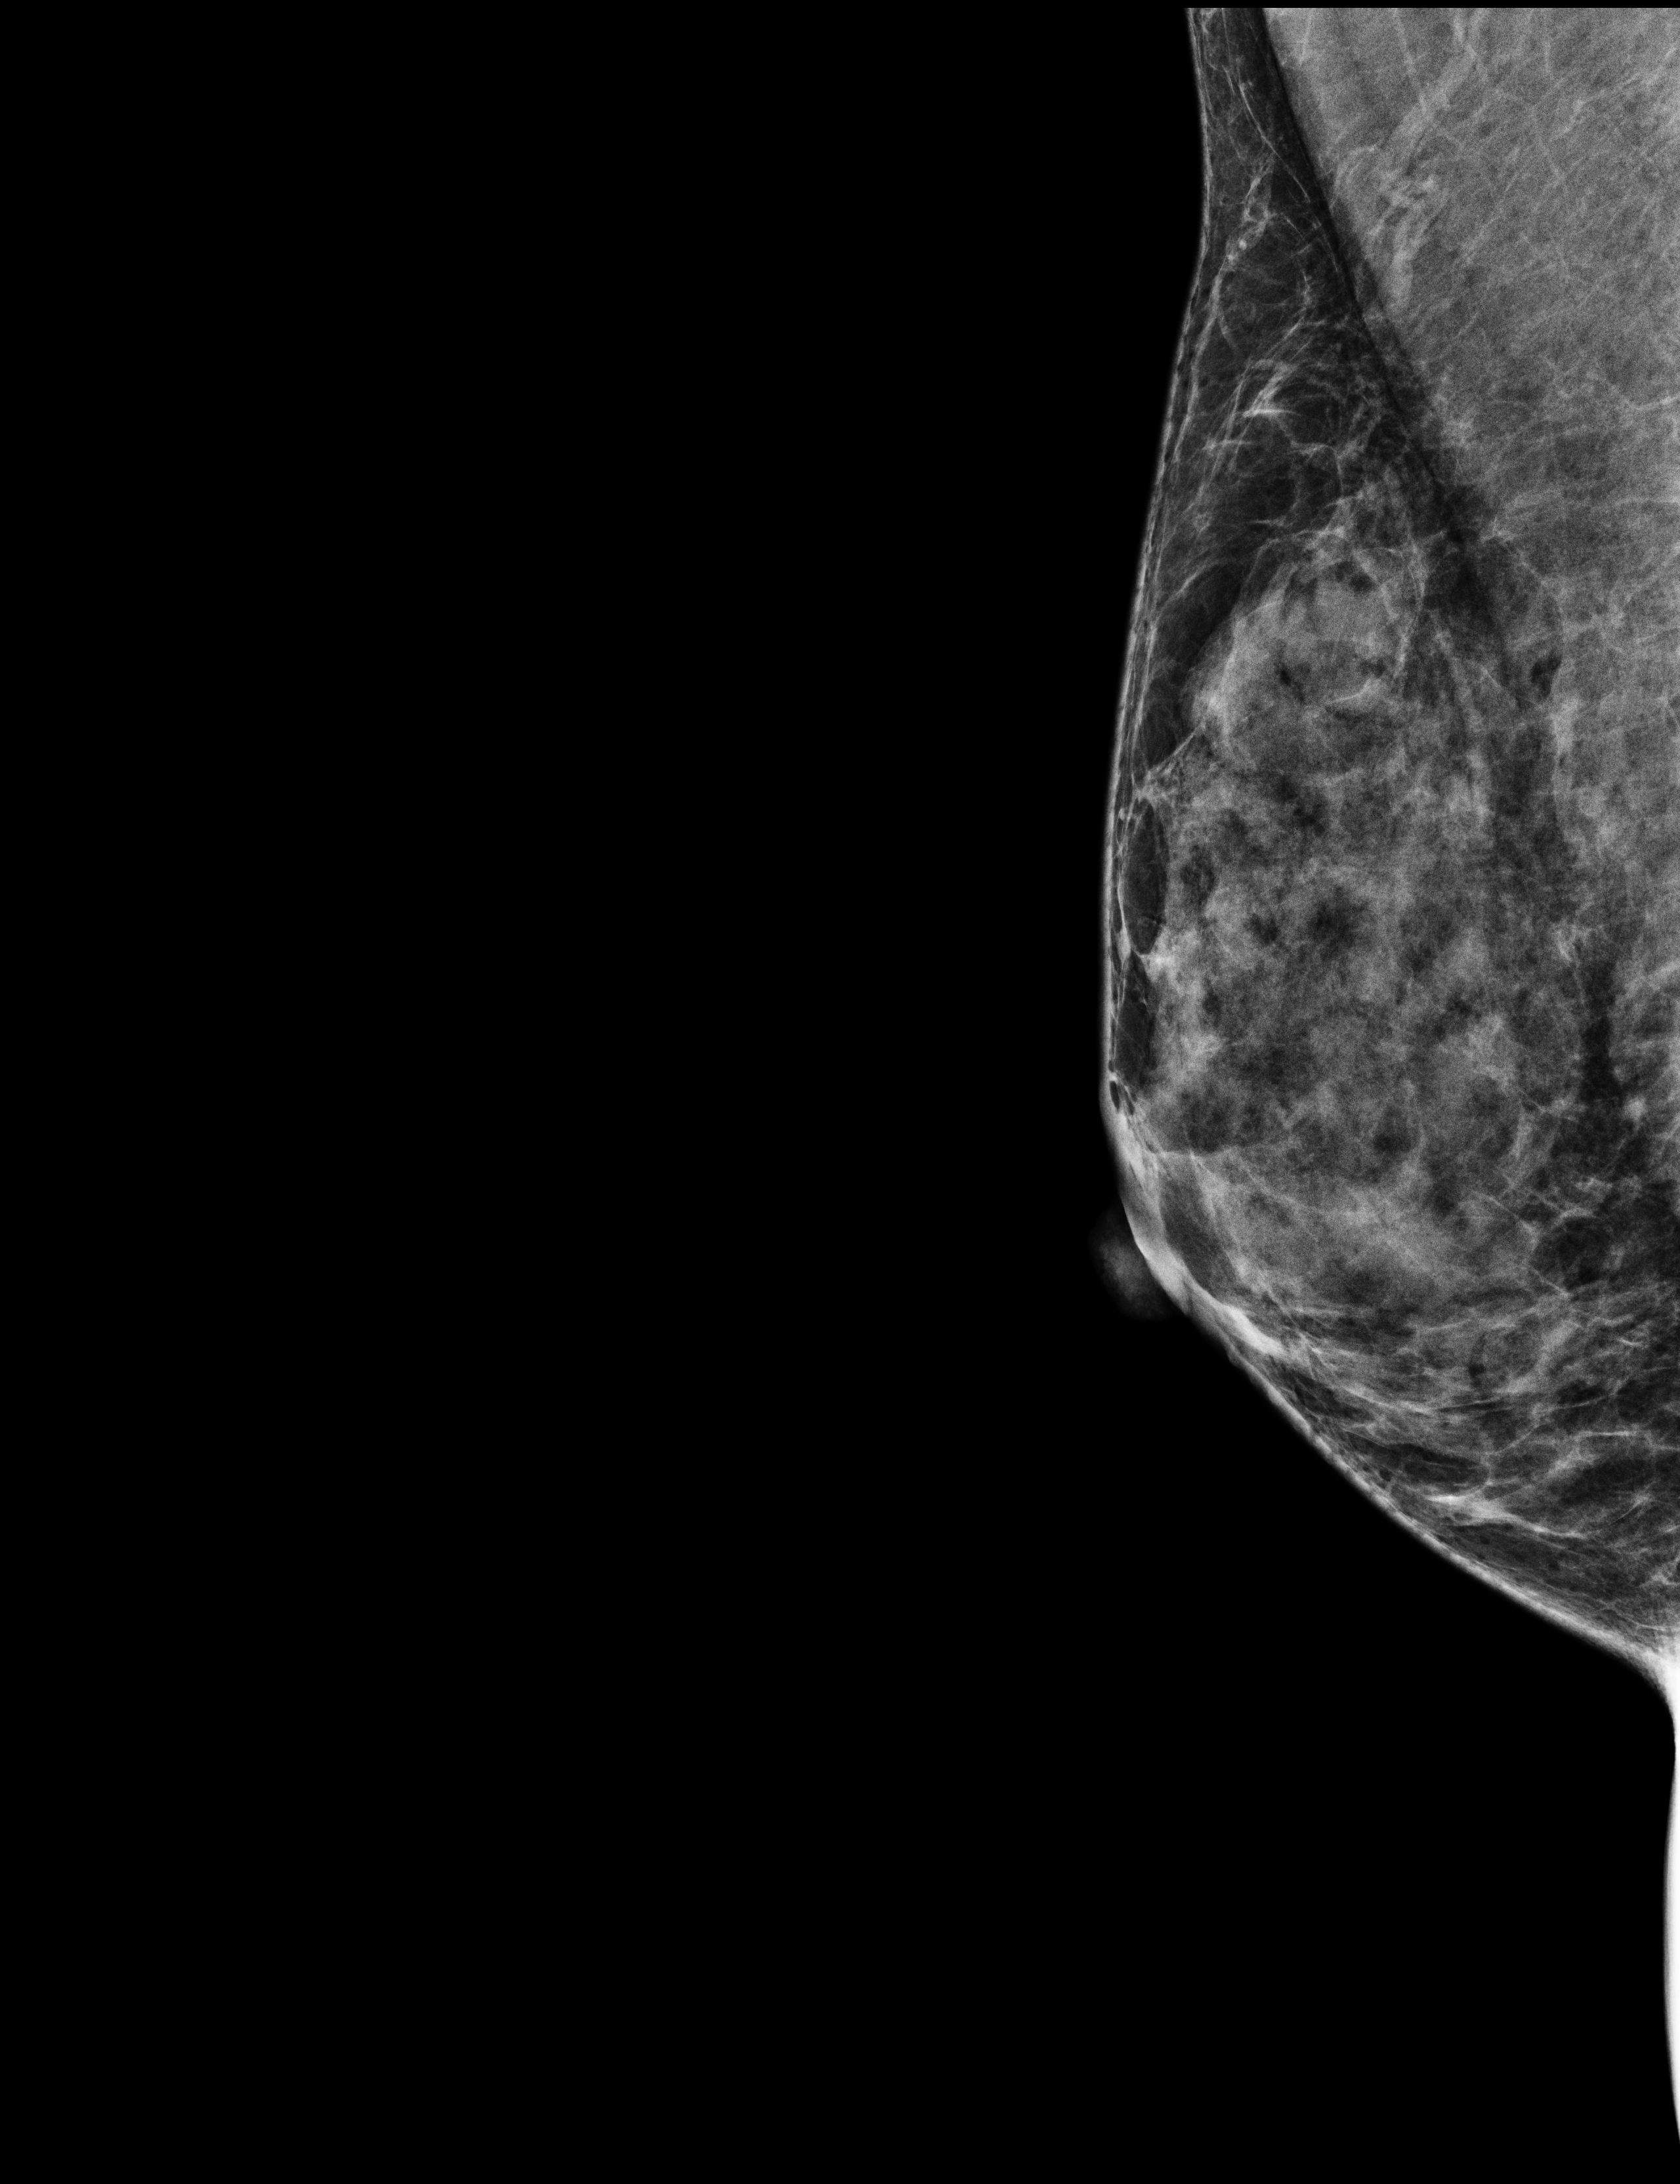
Annual screening mammography examination; compressed breast thickness 34 mm. Patient aged 43 years (female).
Image type: full-field digital mammogram. Breast: right. Projection: mediolateral oblique (MLO) view. BI-RADS breast density category at the screening exam (both breasts, scale 1–4): 3. Final BI-RADS assessment for this screening round (tomosynthesis exam, both breasts): category 2. Recall: no recall after this screen.